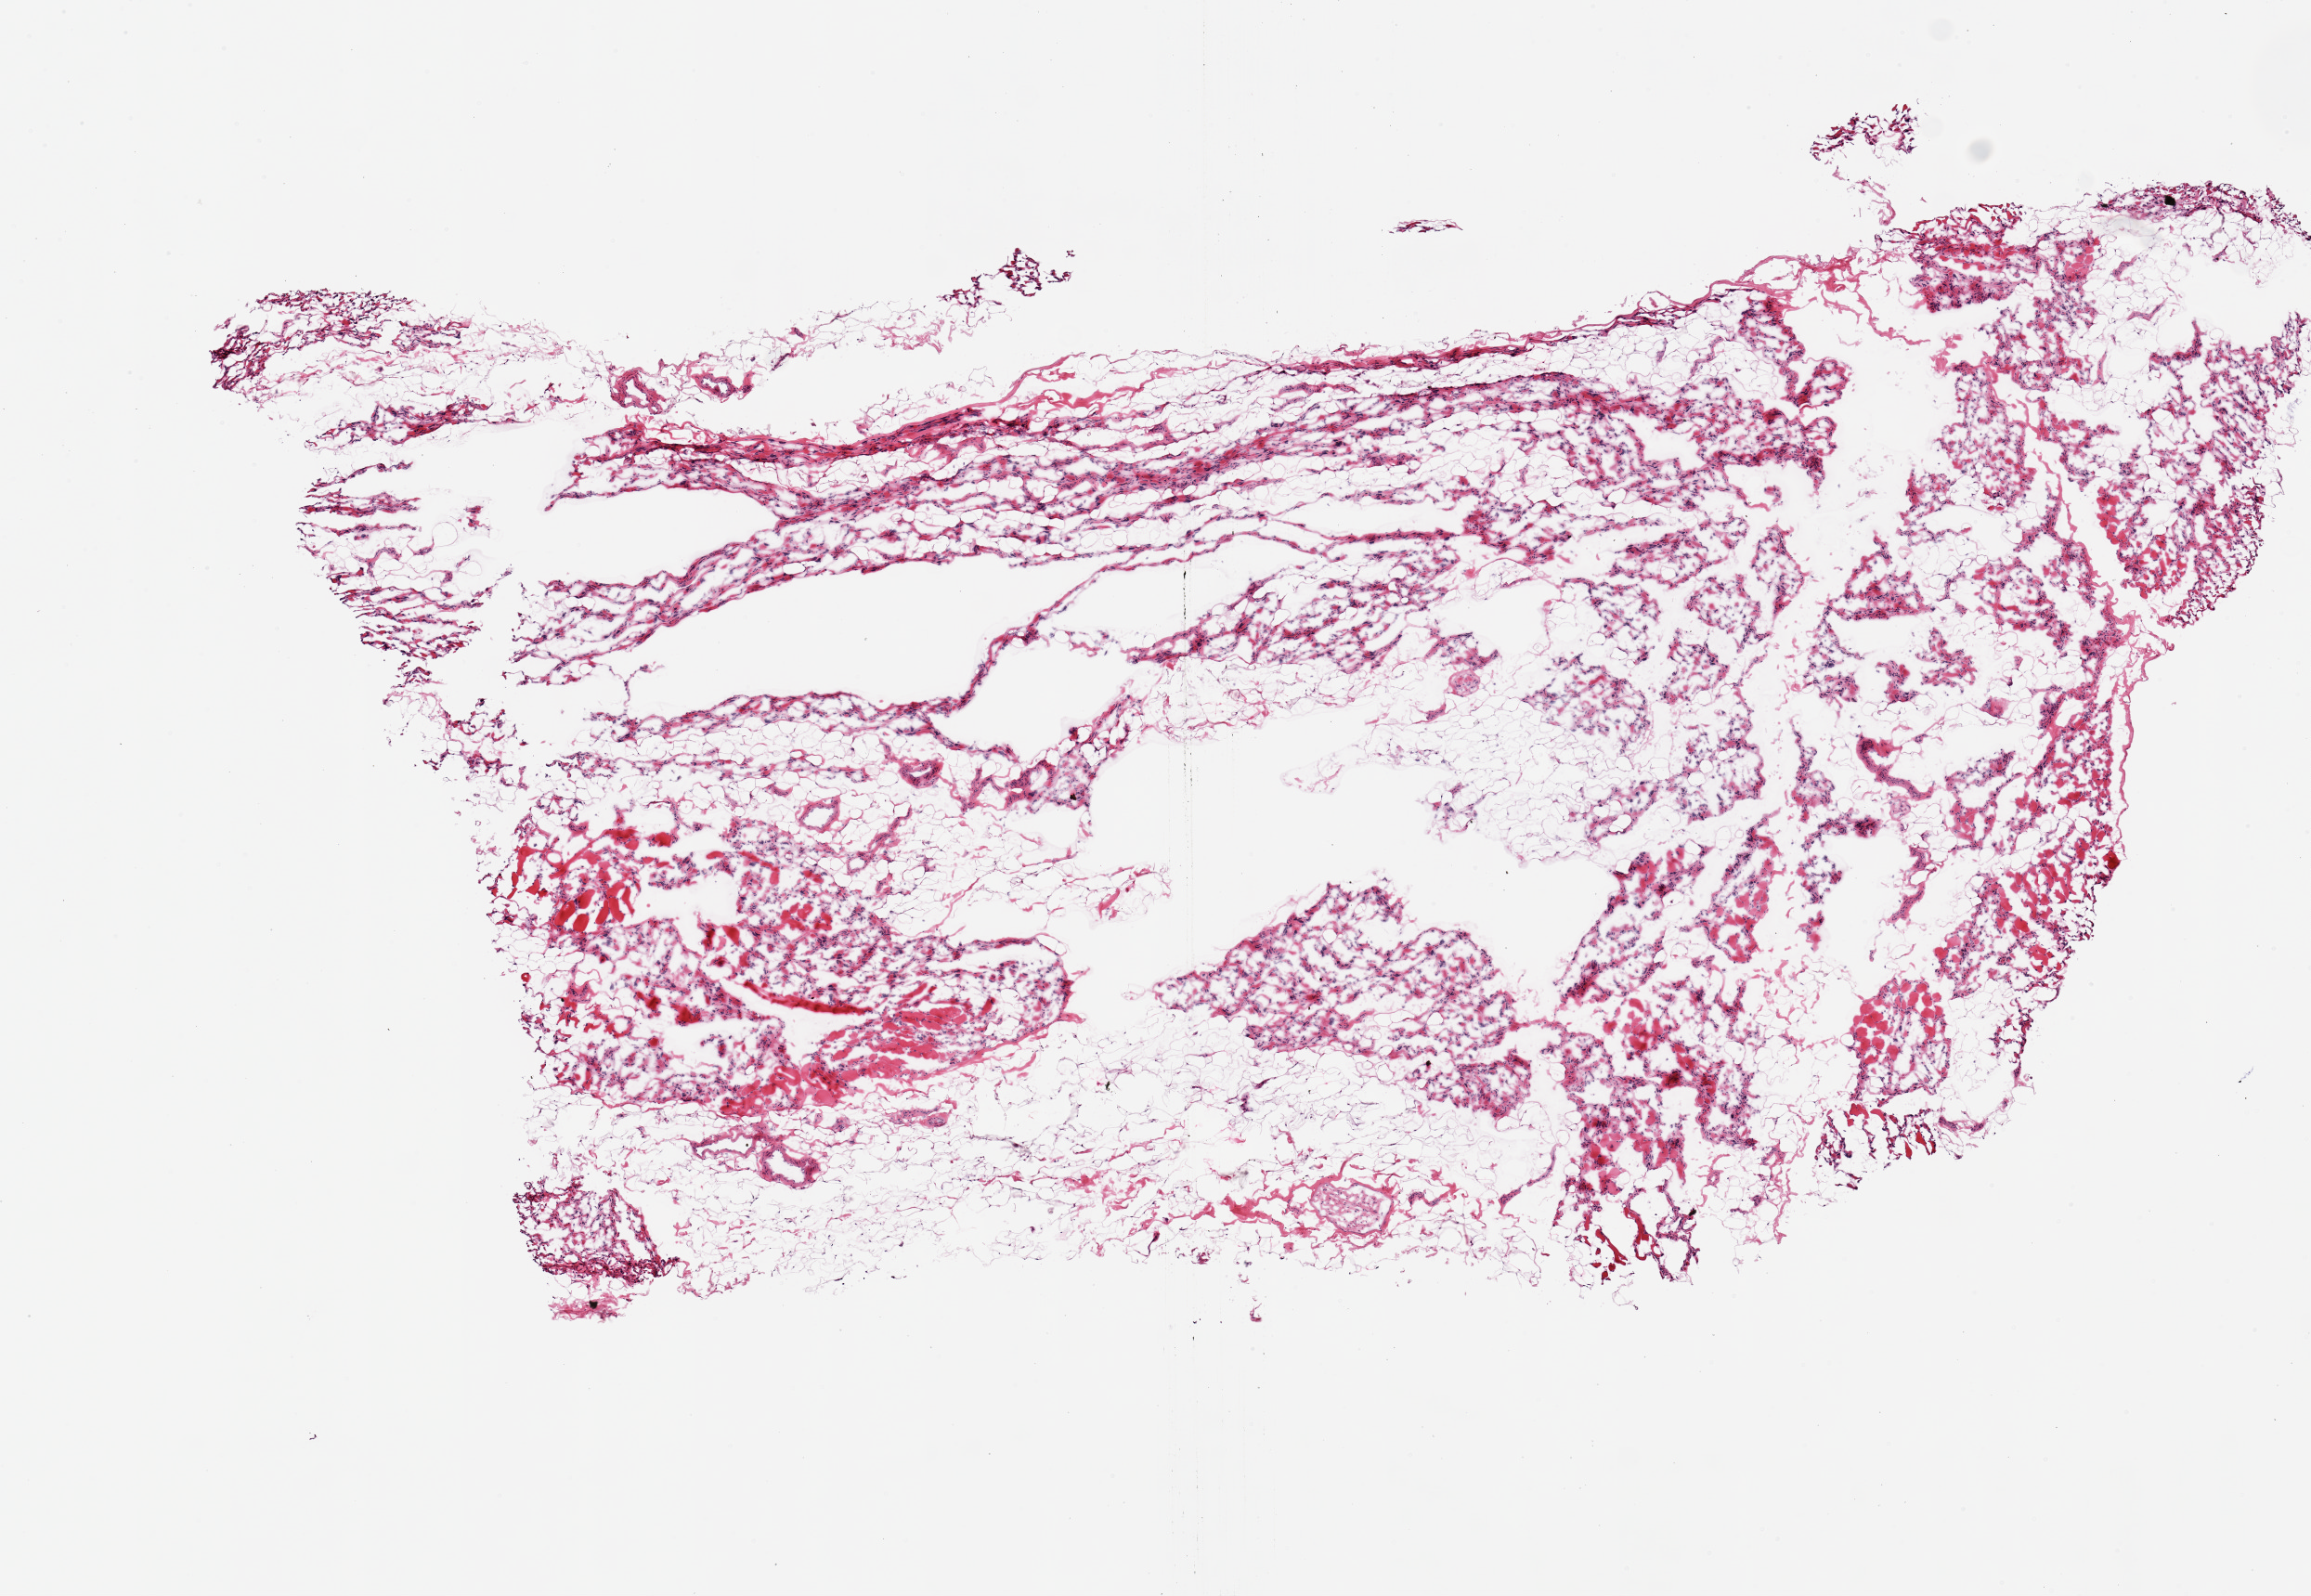
Hematoxylin and eosin (H&E) whole-slide image, brightfield, low-resolution overview of the scanned area, about 9.8 x 6.8 mm (from a 20x scan).
Specimen: frozen section (dry ice); target tissue: skeletal muscle; tissue donor sample.